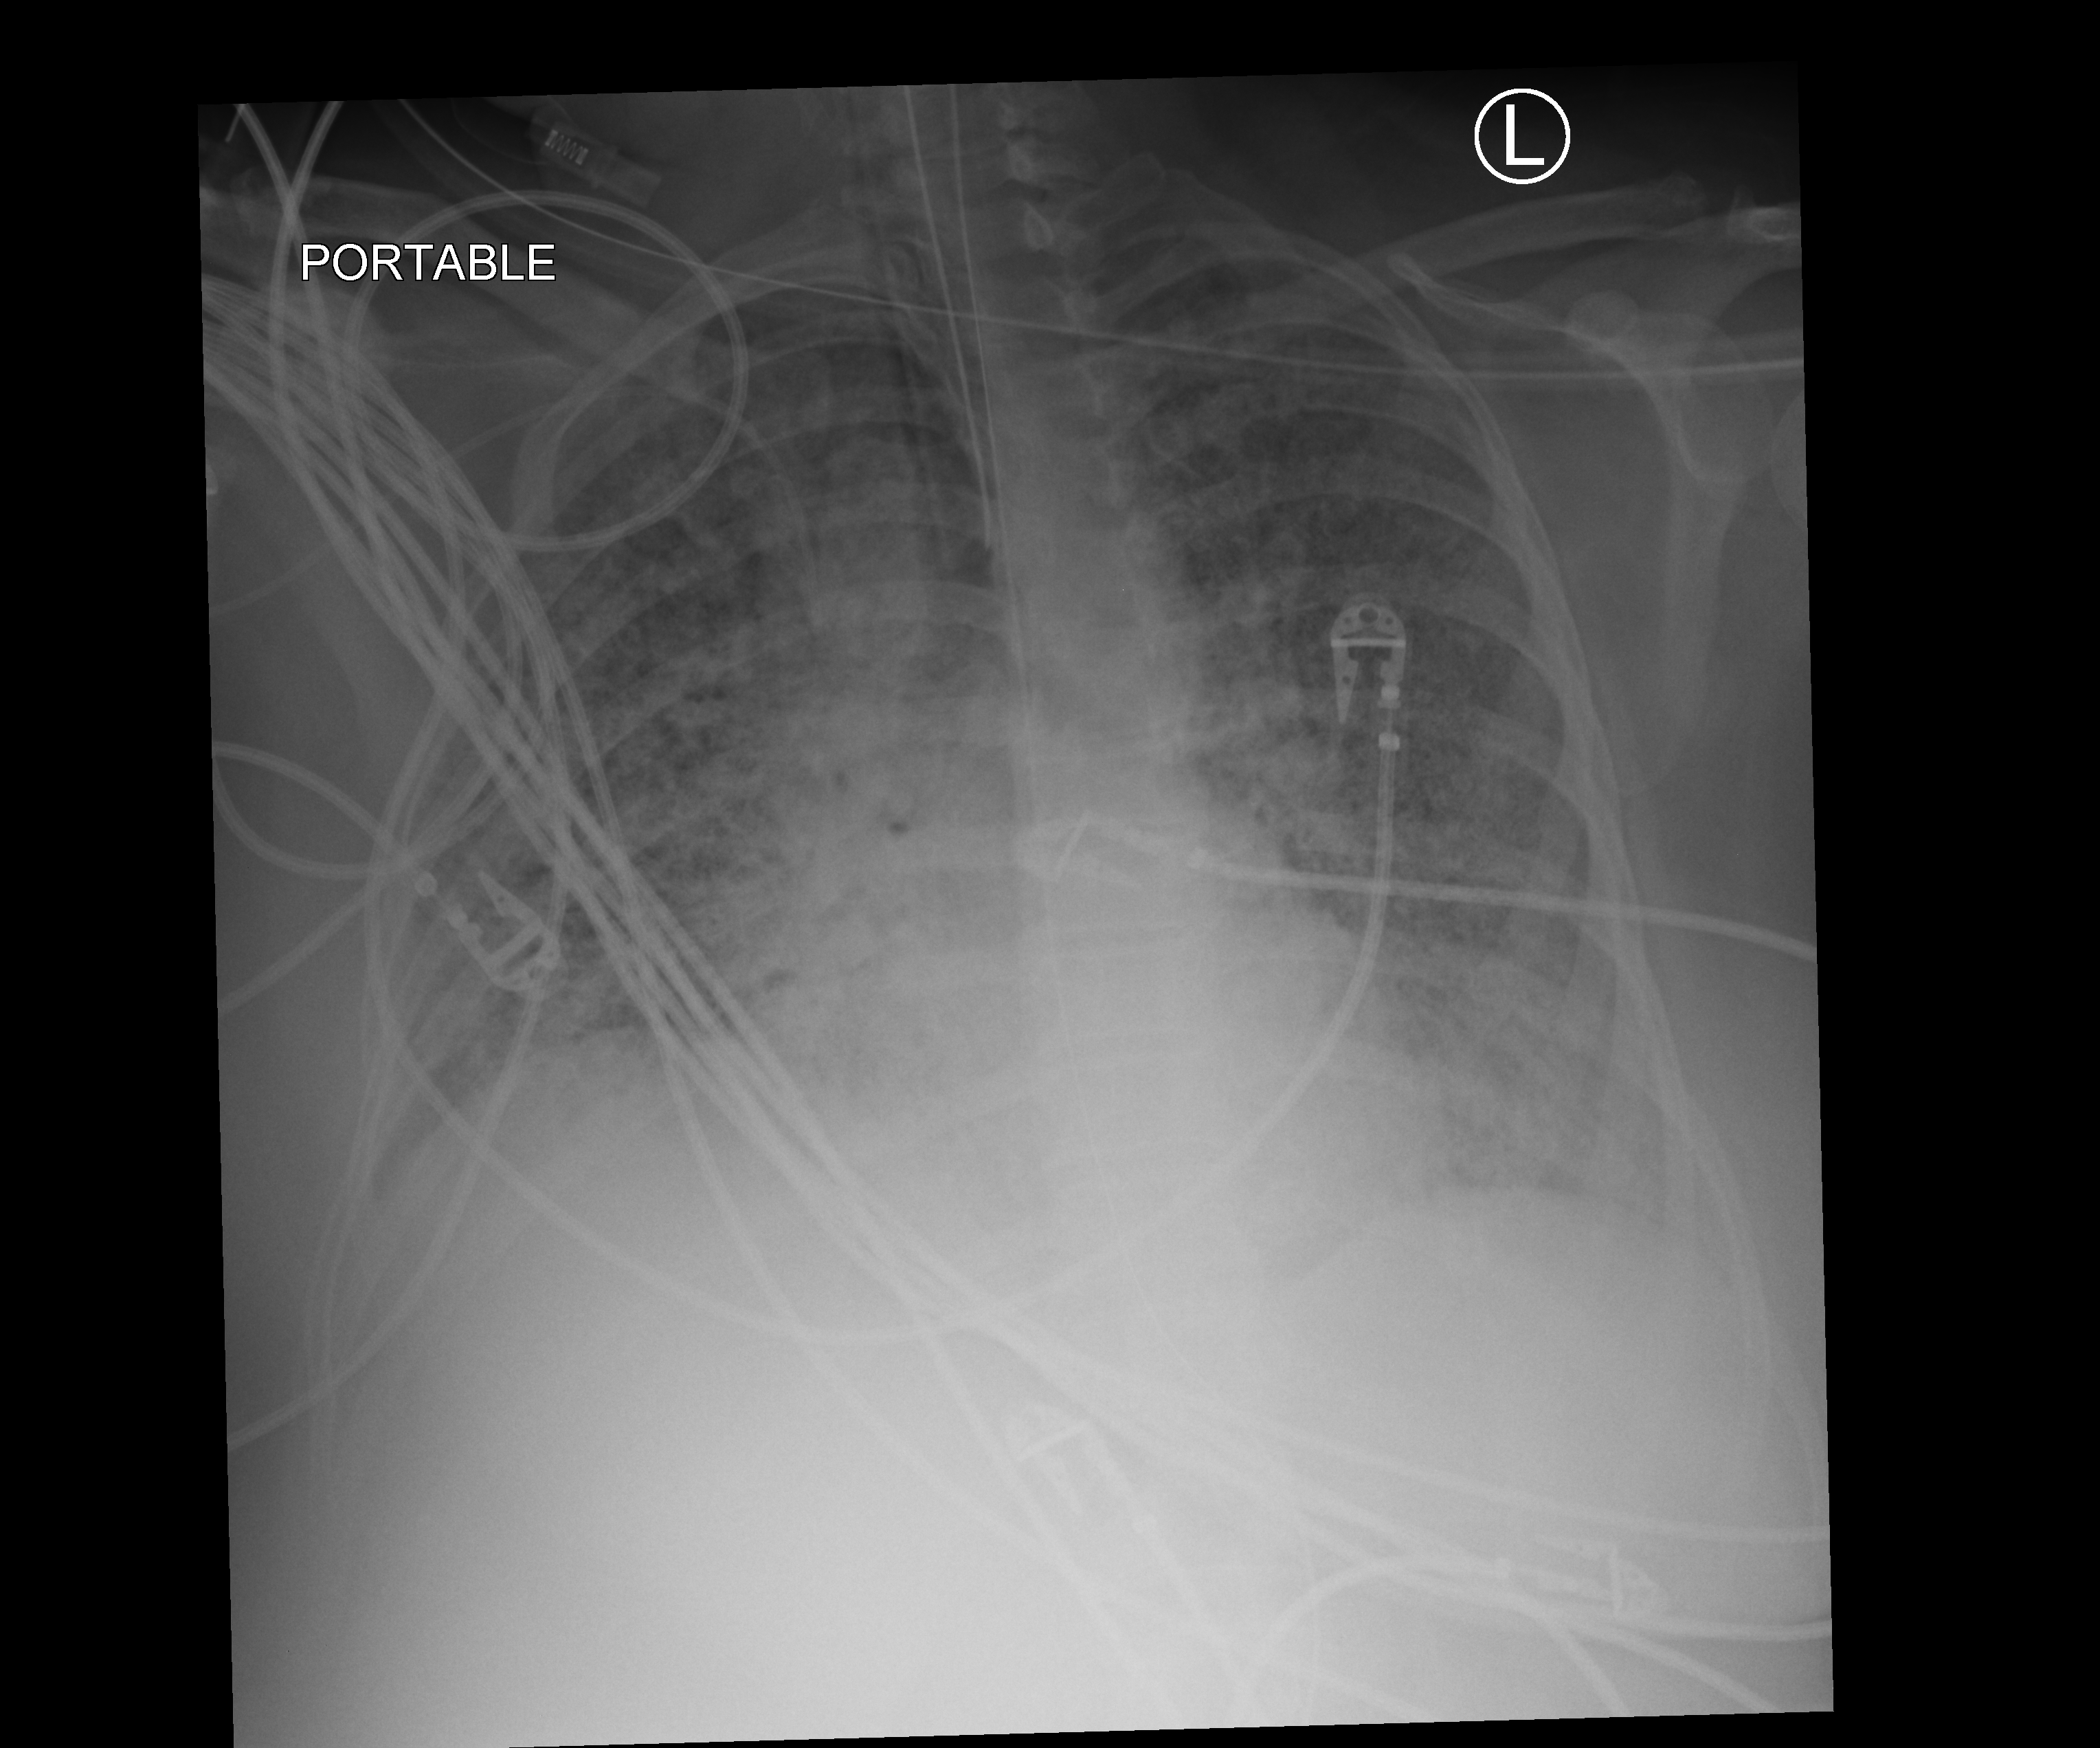
Bedside chest radiograph (computed radiography), anteroposterior (AP) projection. Patient hospitalised with COVID-19; female, aged 18–59 years.
Hospital-stay facts (about this admission, not read from this image; timing relative to this image not recorded): length of hospital stay: 95 days; chronic kidney disease (admission record): no.